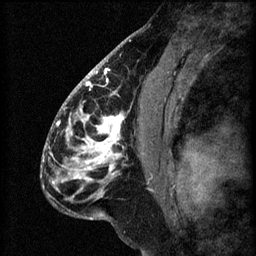
Breast MRI (dynamic contrast-enhanced), one sagittal slice. 3 images stored at this slice position (order not interpretable as contrast timing). 1.5 T. TE 4.2 ms, TR 8.2 ms. 2.2 mm slice thickness. 256 × 256 image matrix, field of view 180 × 180 mm. Patient: female, 41 years.
Outlined on this slice (semi-automatically segmented with operator editing):
- analysis volume of interest (the breast-tissue region the enhancement analysis was run in; not a lesion): box from (x=56, y=104) to (x=157, y=207) px
- tumour enhancement mask (voxels above the 70 % enhancement threshold inside the analysis volume of interest): (x=61, y=108)–(x=124, y=199)